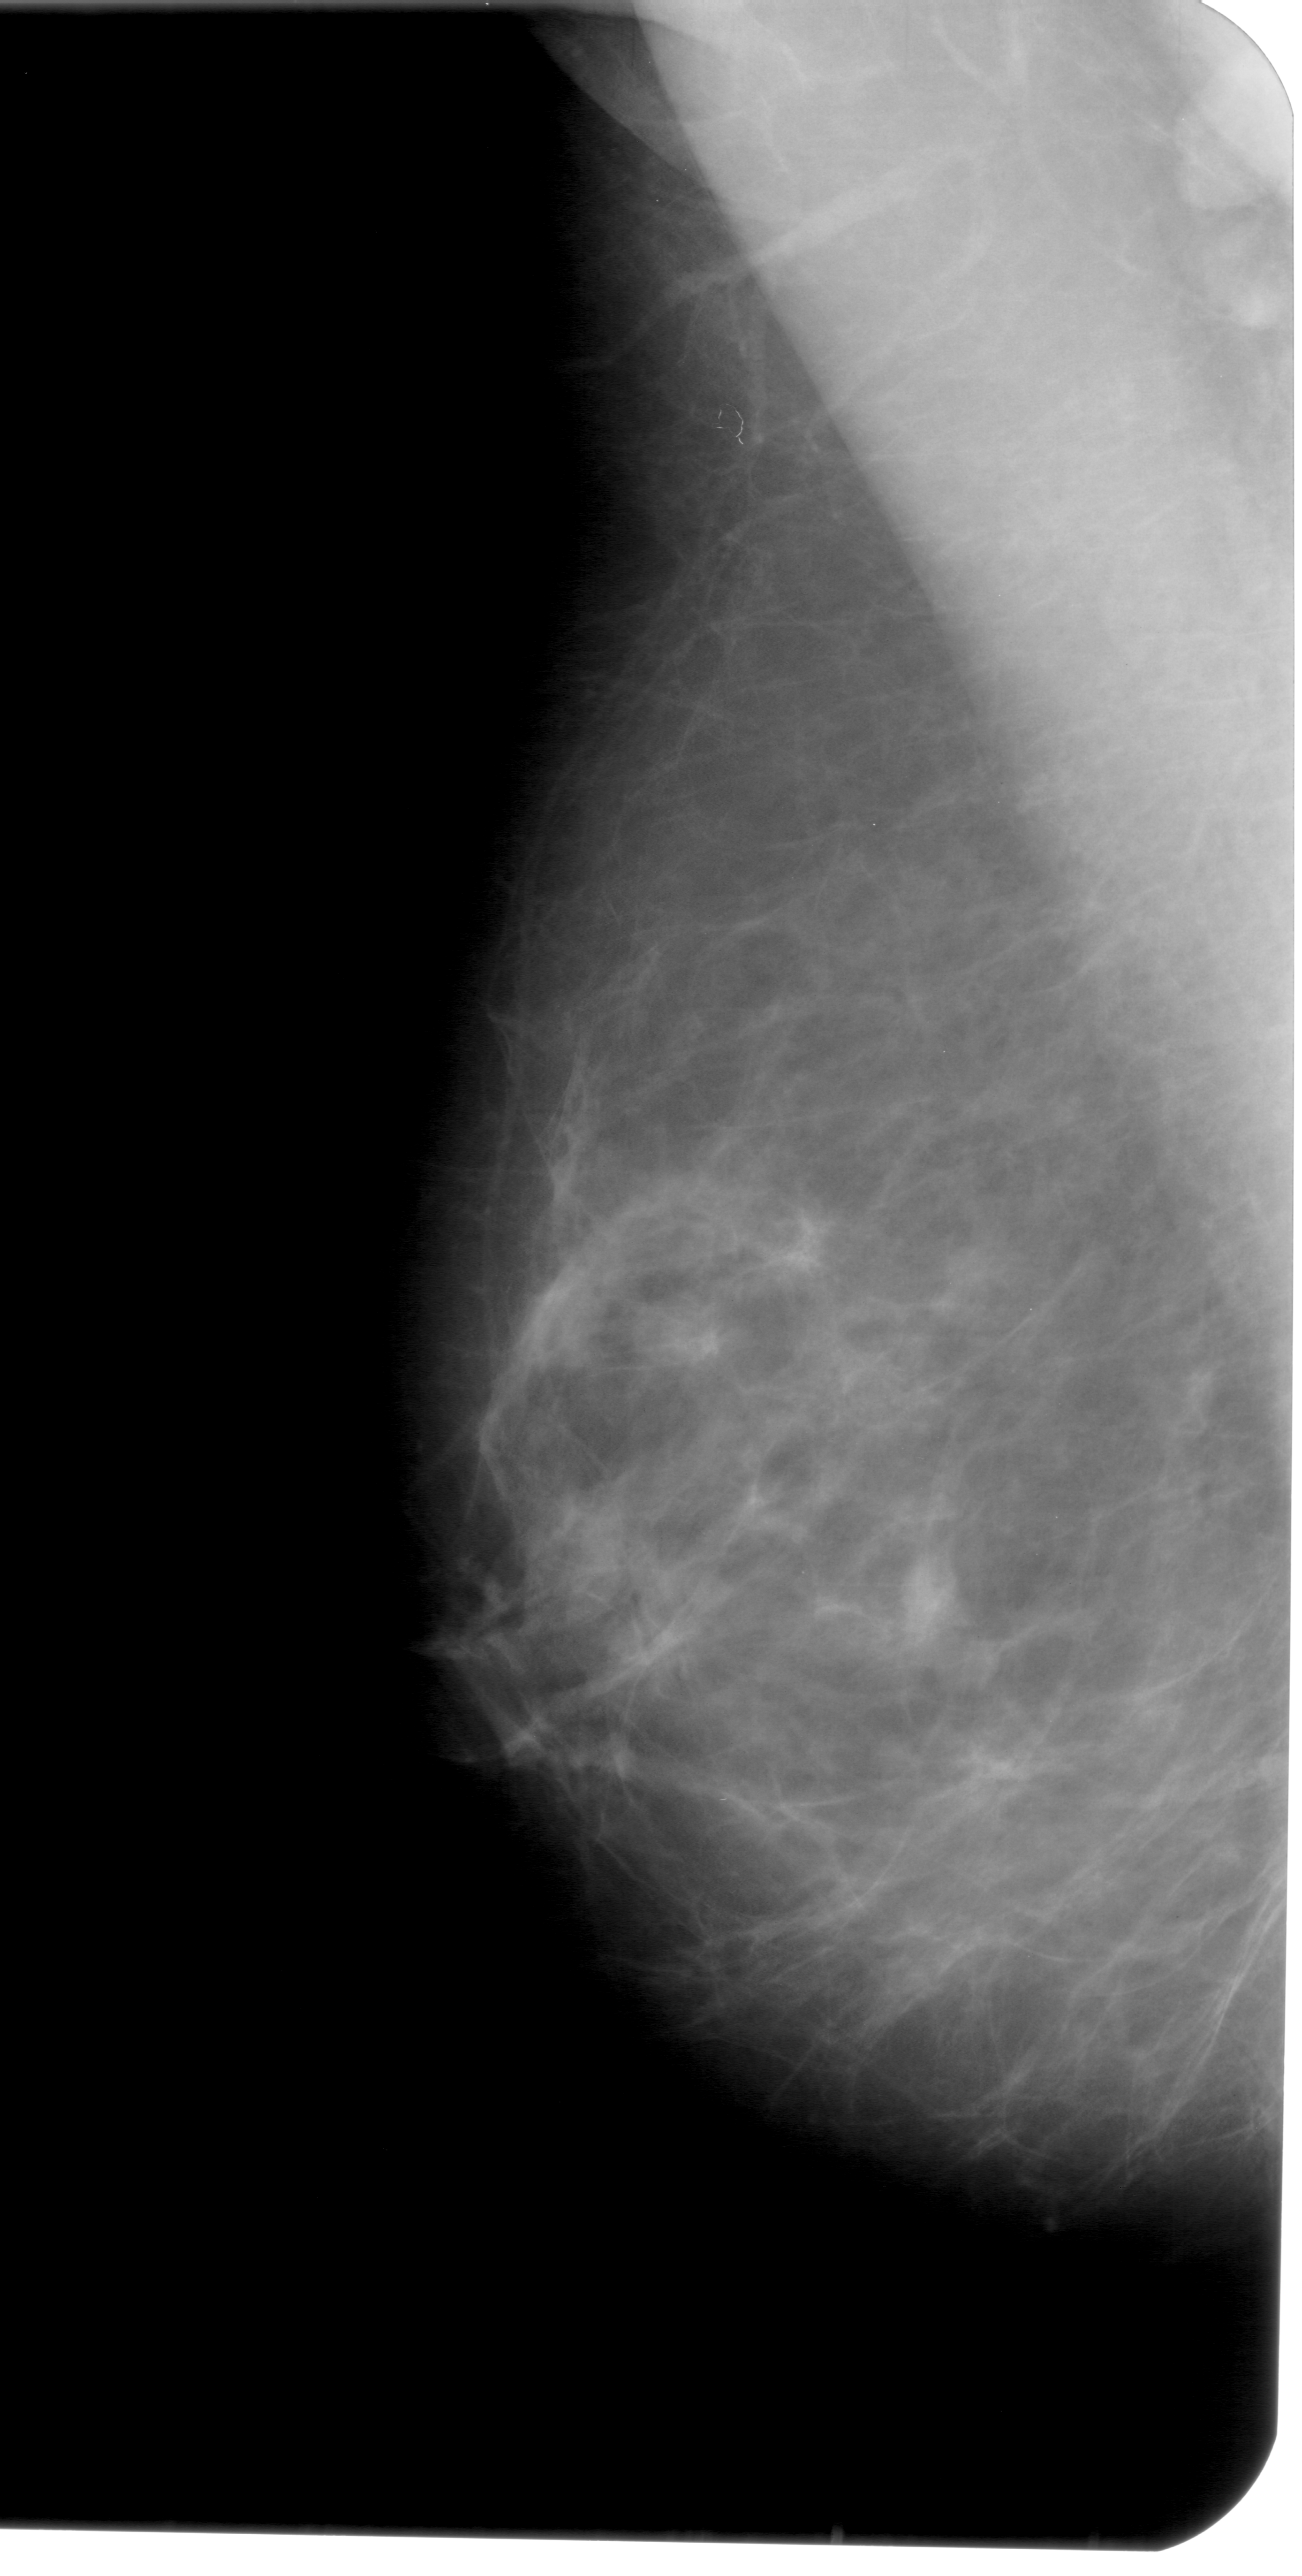
Mammogram (digitized film). Left breast. MLO view. BI-RADS breast density category 2 (scale 1–4). 1302 × 2576 image matrix.
Expert-marked regions of interest on this image (one box per marked abnormality):
- mass, shape irregular, margins ill defined; BI-RADS assessment category 4; subtlety rating 3 on a 1 (subtle) to 5 (obvious) scale; pathology result (as recorded, not read from the image): benign: bounding box [x1, y1, x2, y2] px = [883, 1552, 973, 1670]